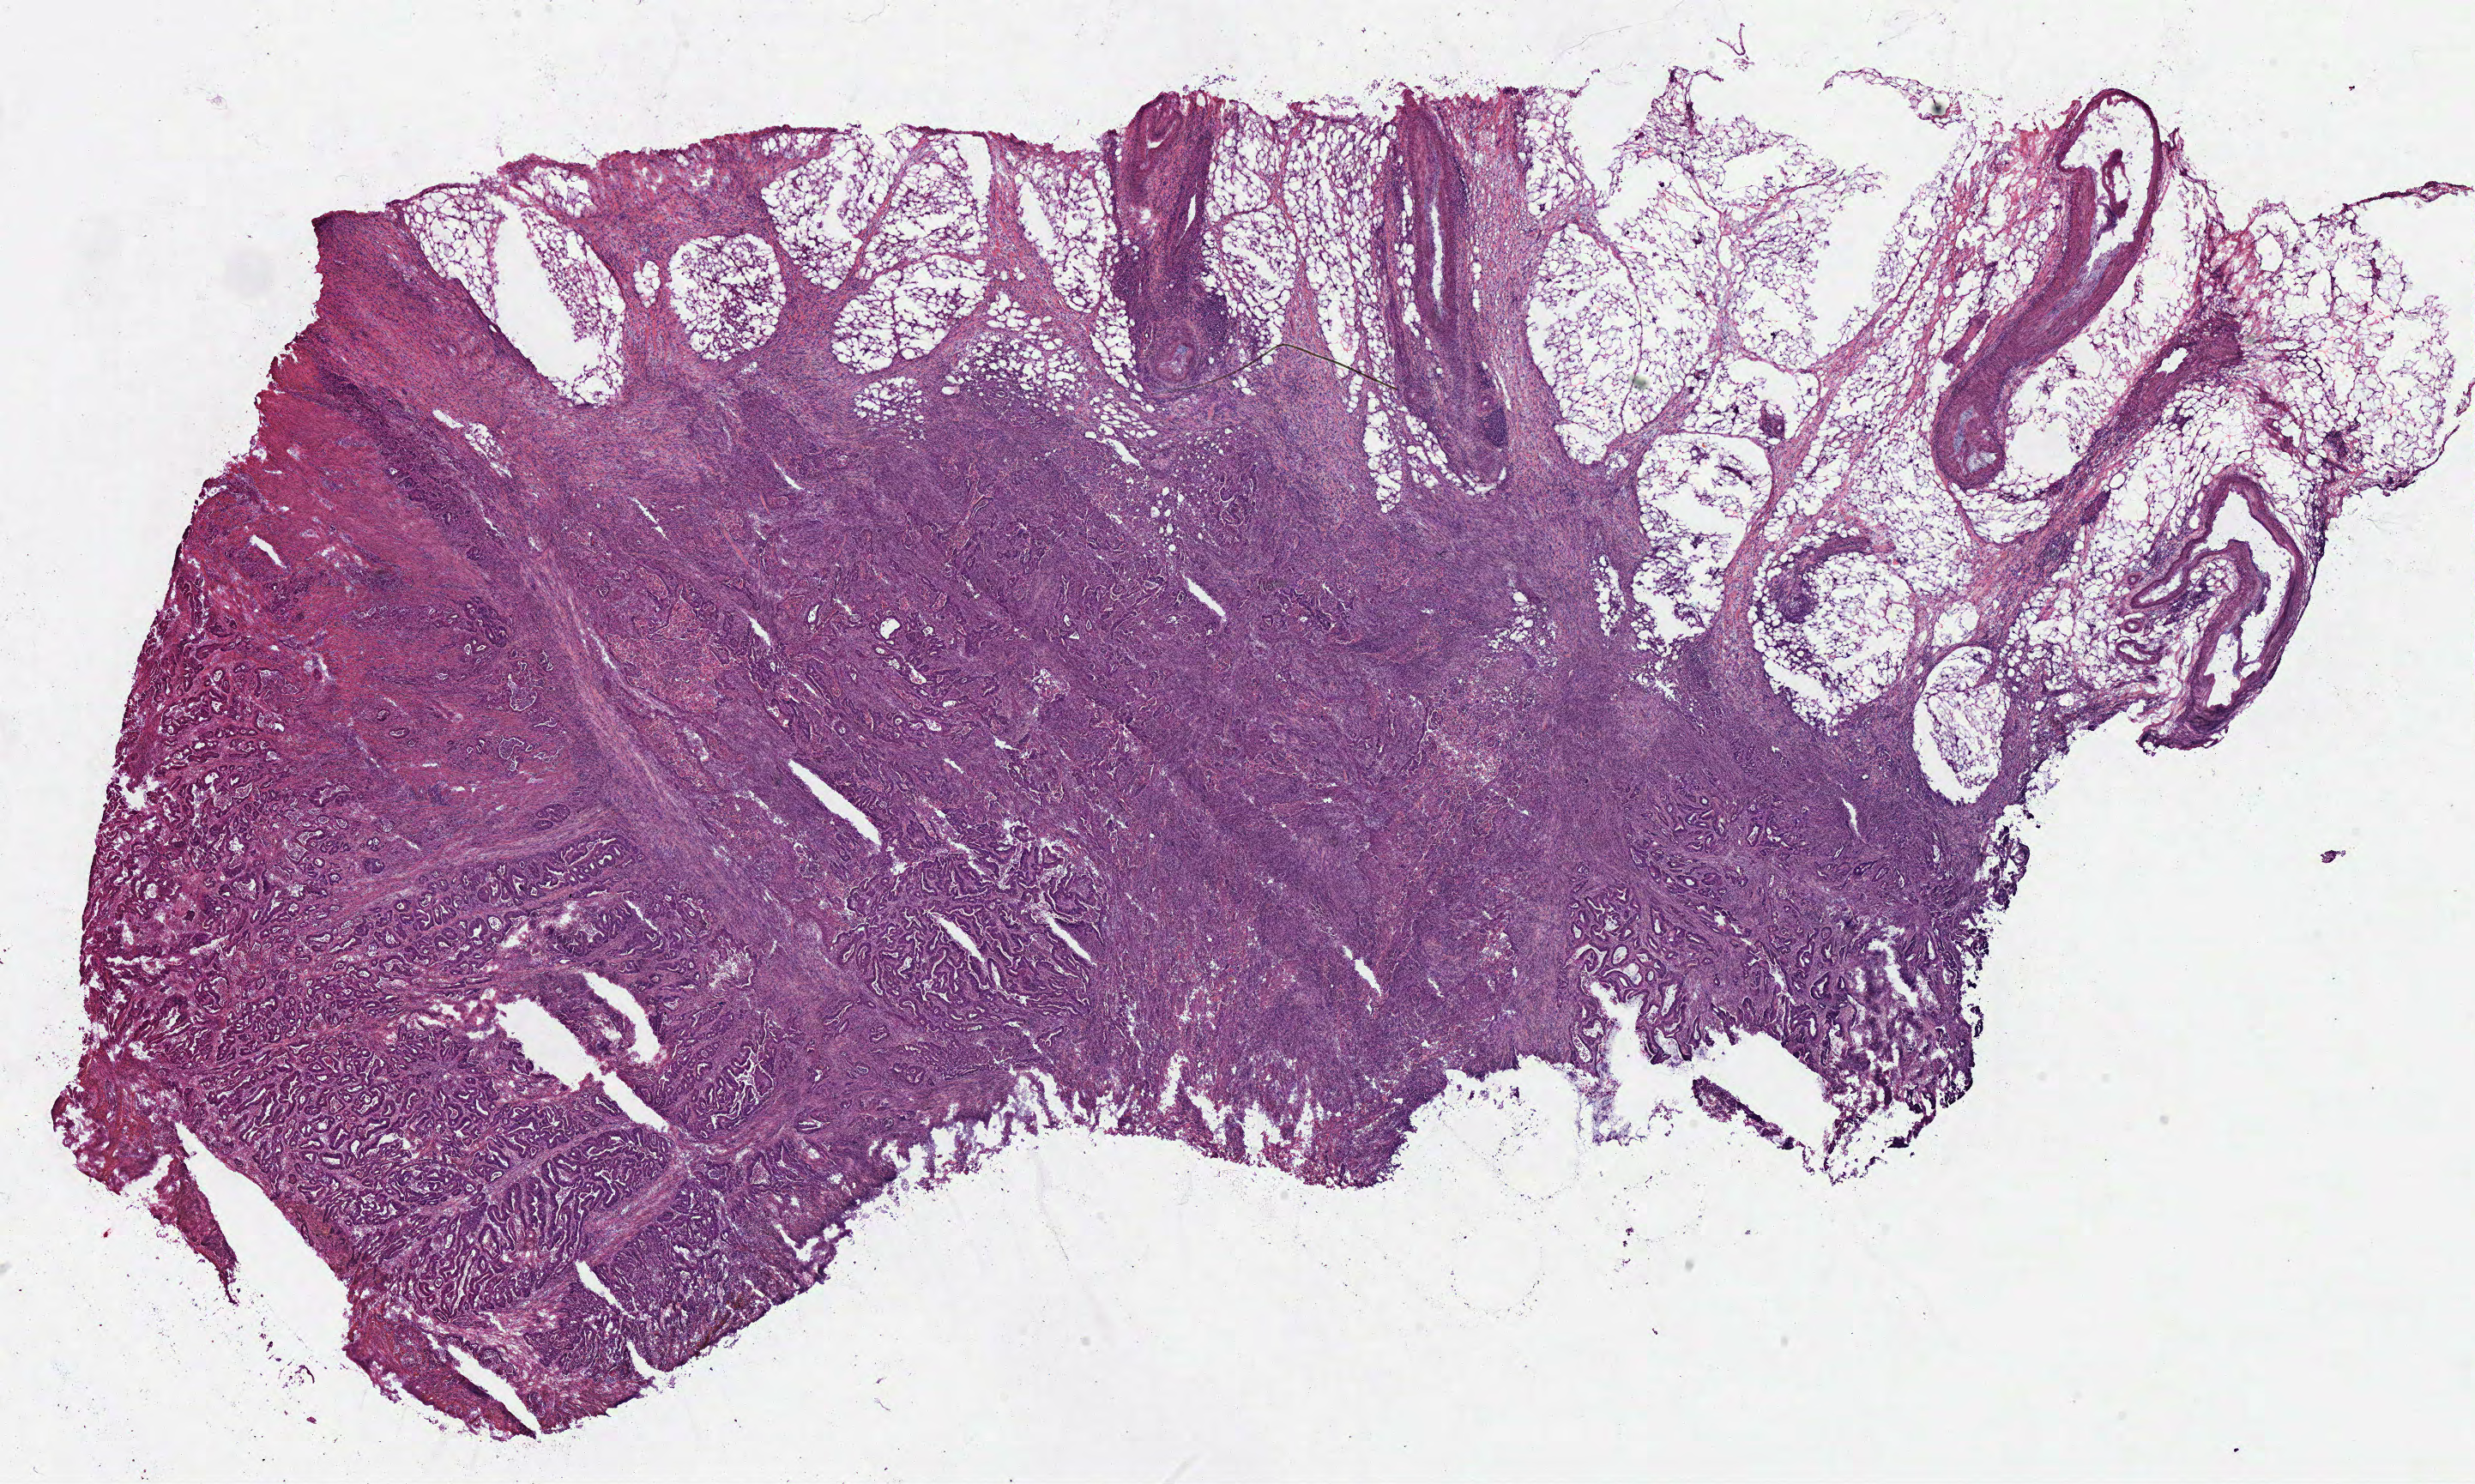
H&E-stained whole-slide image, low-resolution overview of the scanned area, about 22.7 x 13.6 mm (from a 40x scan), frozen section from the bottom of the tissue portion, sample: primary tumour, colon. Male patient; age at initial diagnosis 64 years. Slide review estimates, as recorded: tumour cells 70%, tumour nuclei 70%, normal cells 0%, stromal cells 25%, necrosis 5%.
AJCC pathologic stage: IIA (7th edition). Pathologic diagnosis: Adenocarcinoma, NOS (ascending colon).